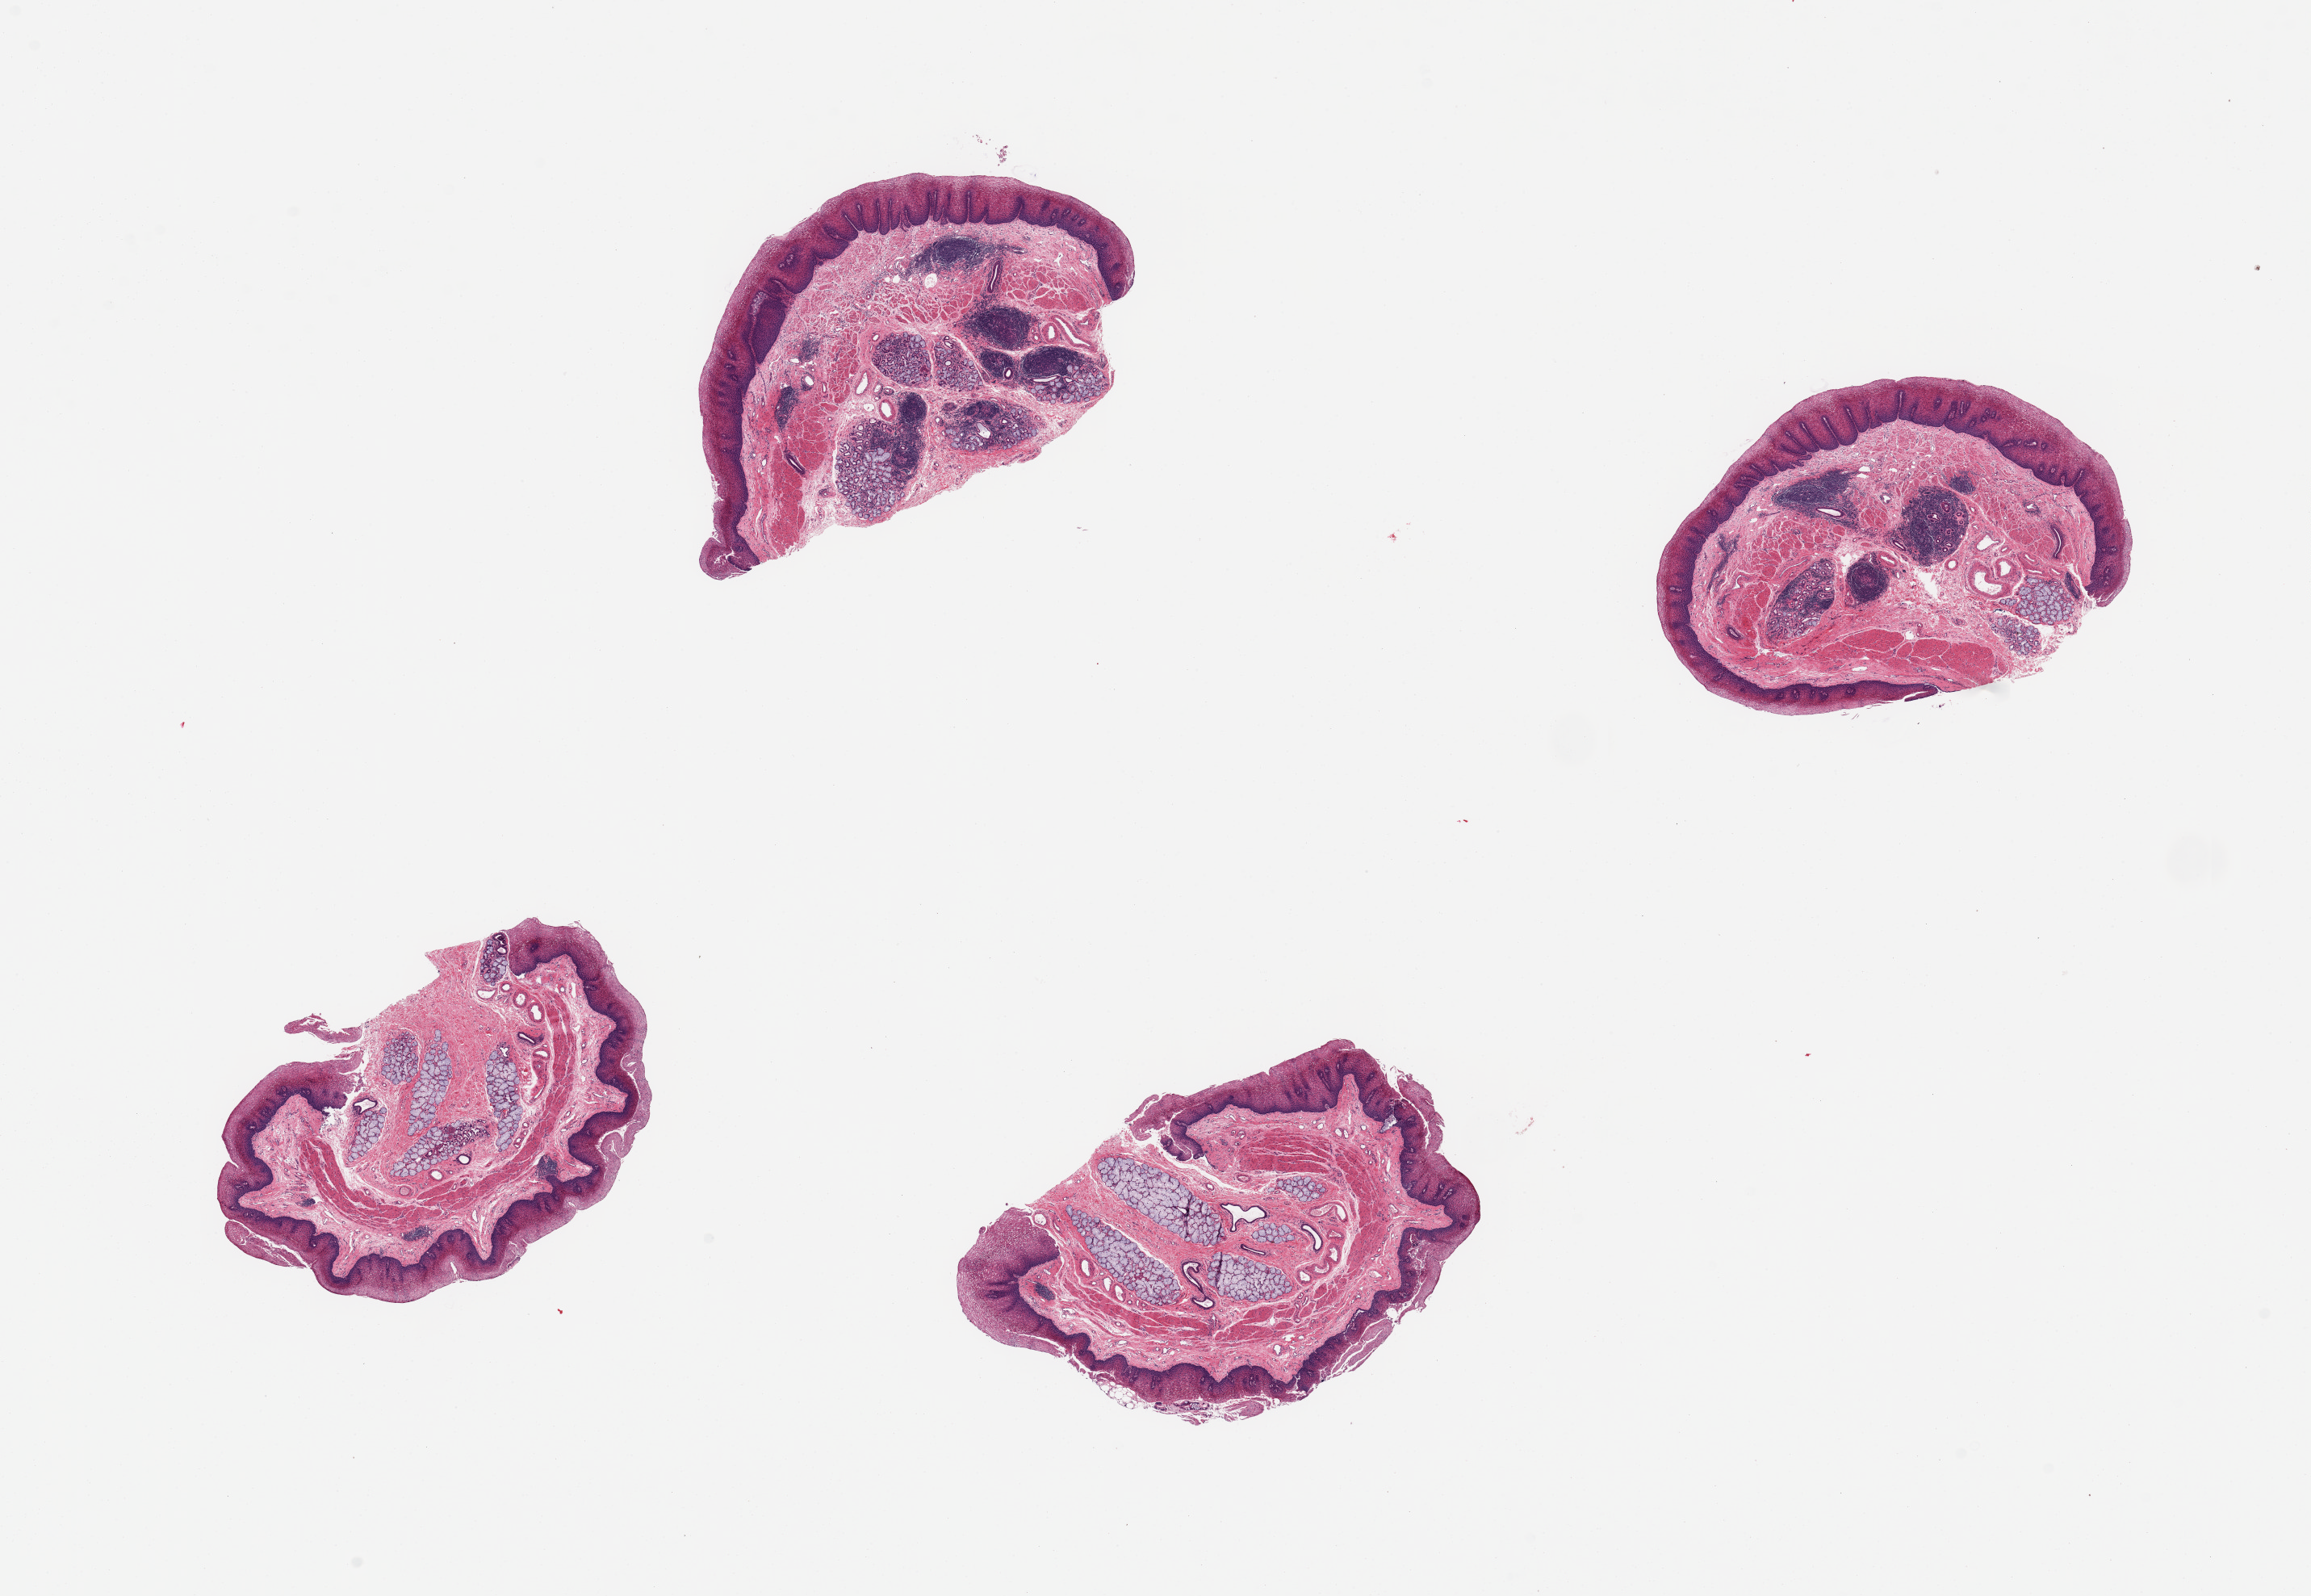
Digitized H&E-stained section, a low-resolution overview of the entire scanned area, about 22.6 x 15.6 mm, PAXgene-fixed paraffin-embedded (PFPE) section, sampled site (target tissue): esophageal mucous membrane, donor tissue sample. Male donor.
Review note (as recorded): 4 pieces; squamous hyperplasia and chronic inflammation especially in subepithelial glands (elevated lymphoid content) in 2 of 4 pieces.